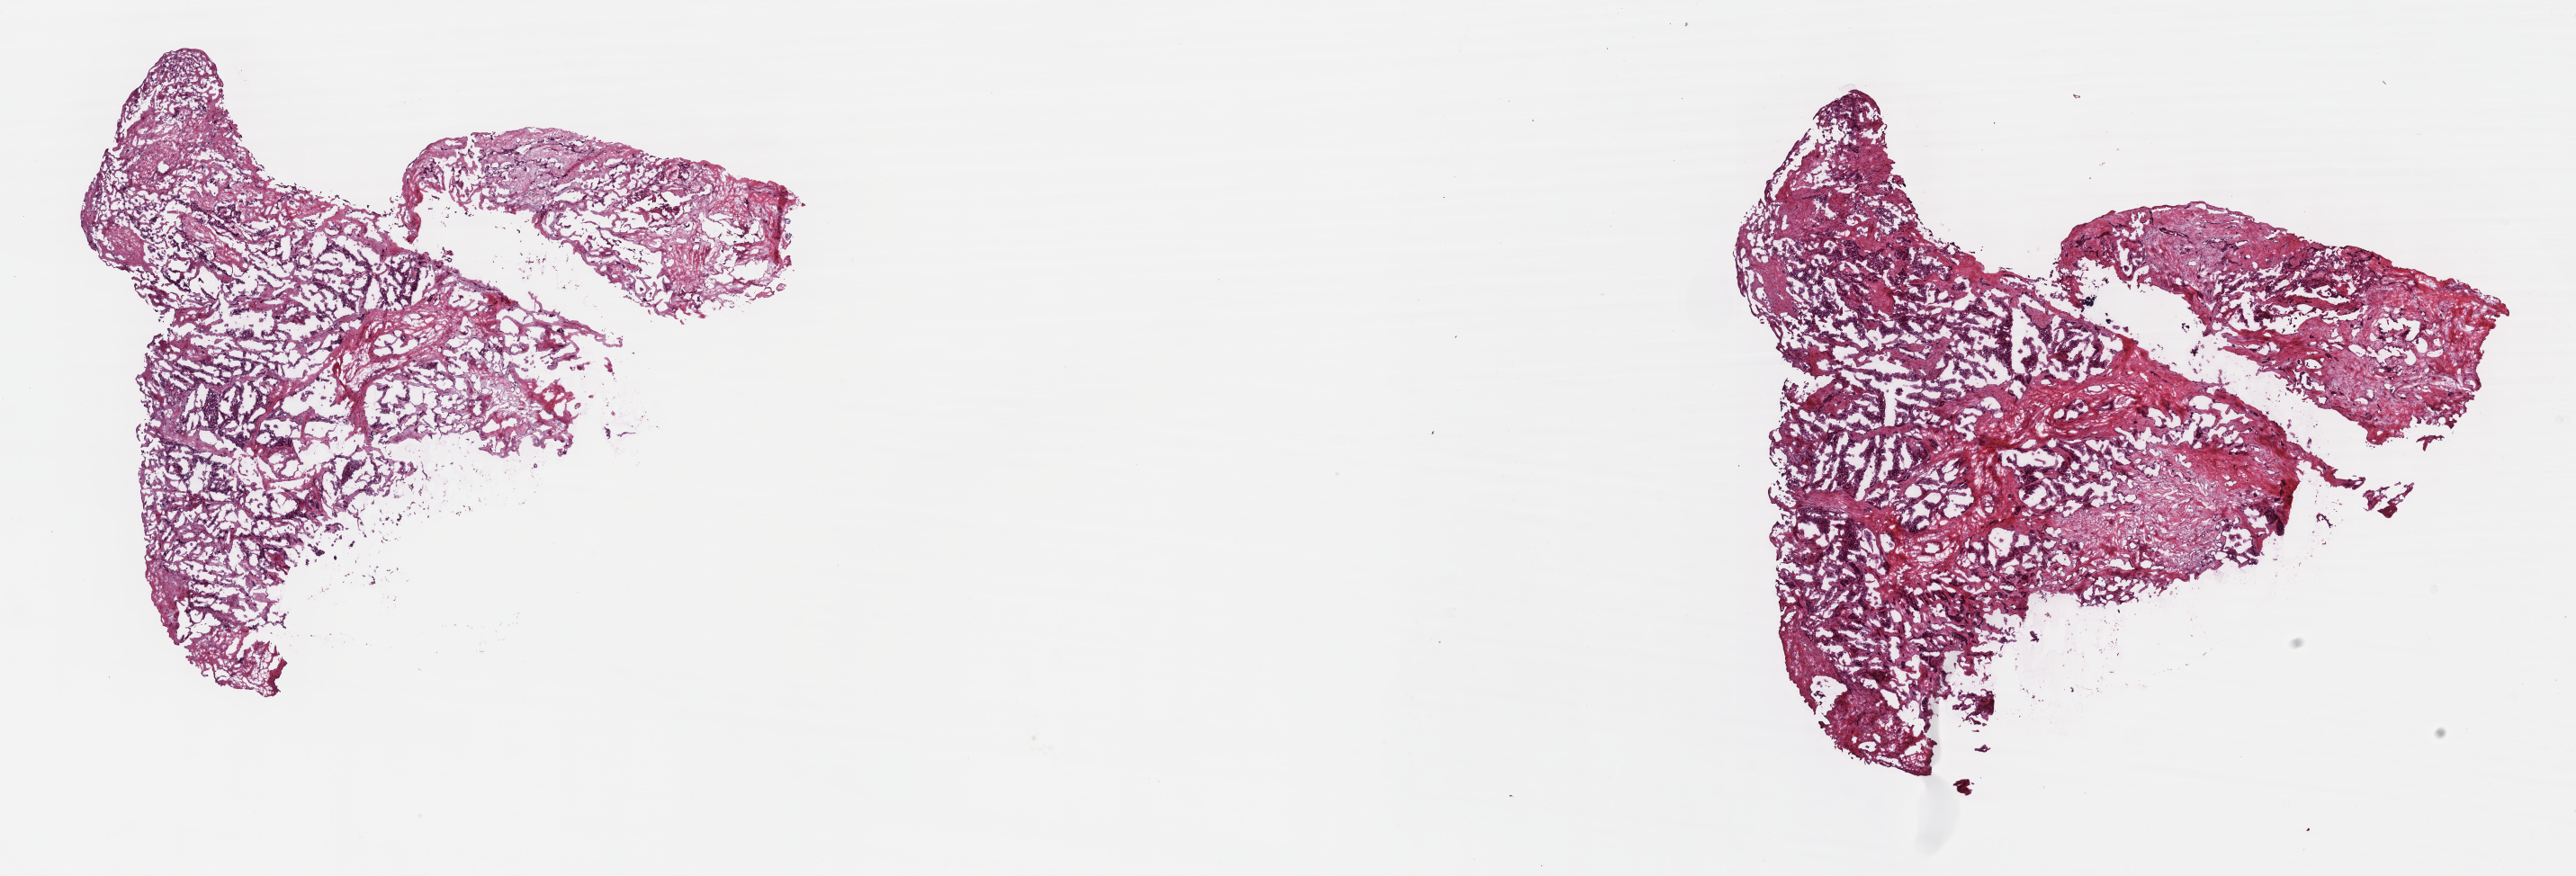
Digitized H&E tissue section (whole slide), low-resolution overview of the scanned area, about 23.2 x 7.9 mm (slide scanned at 40x). Frozen section from the top of the tissue portion. Bile duct, primary tumour sample. Female, age 71 years at initial diagnosis. Histologic grade: G2 (moderately differentiated). Composition of this section per pathologist review: tumour cells 45%, tumour nuclei 90%, normal cells 0%, stromal cells 40%, necrosis 15%. Inflammatory infiltration, as recorded: lymphocyte infiltration 4%, monocyte infiltration 0%, neutrophil infiltration 0%.
• pathologic diagnosis: Cholangiocarcinoma (intrahepatic bile duct)
• AJCC pathologic stage: II (7th edition)
• TNM: T2a N0 M0